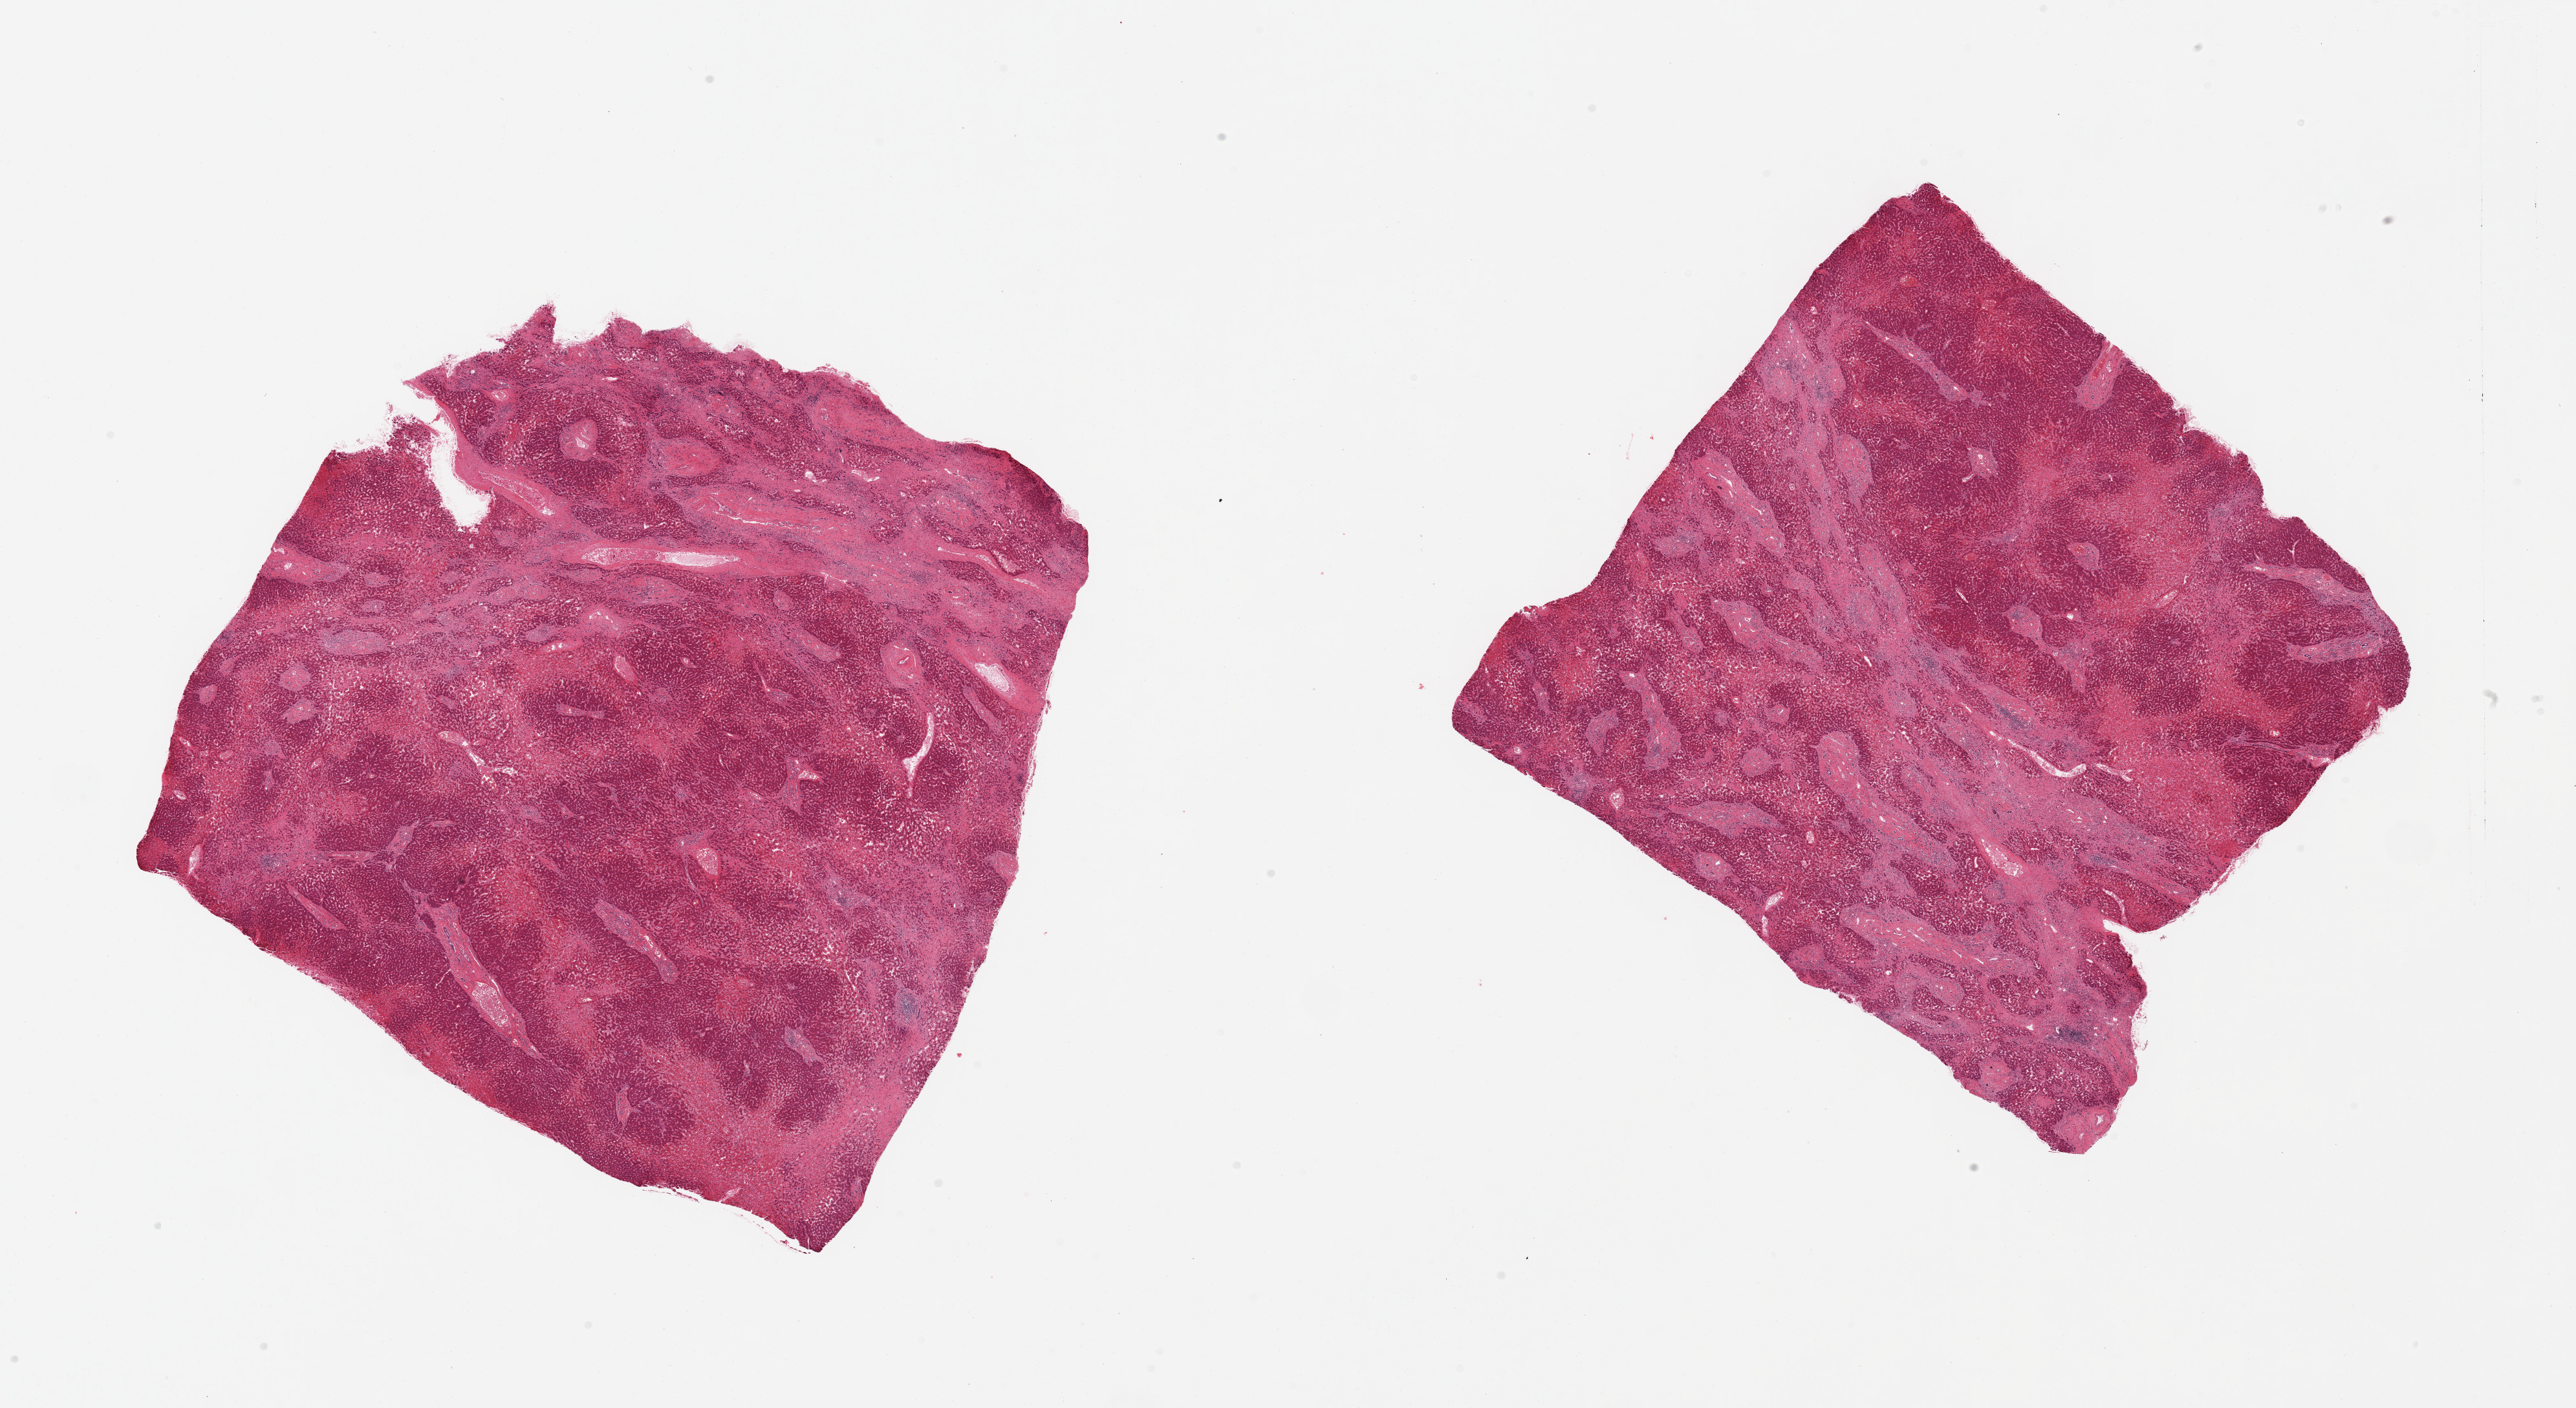
Digitized haematoxylin and eosin-stained section — a low-resolution overview of the entire scanned area, about 31.5 x 17.2 mm. PAXgene-fixed paraffin-embedded (PFPE) section. Target tissue: liver. Tissue donor sample. Donor sex: male.
Review note (as recorded): 2 pieces, severe chronic congestive damage/fibrosis, 'cardiac cirrhosis'.